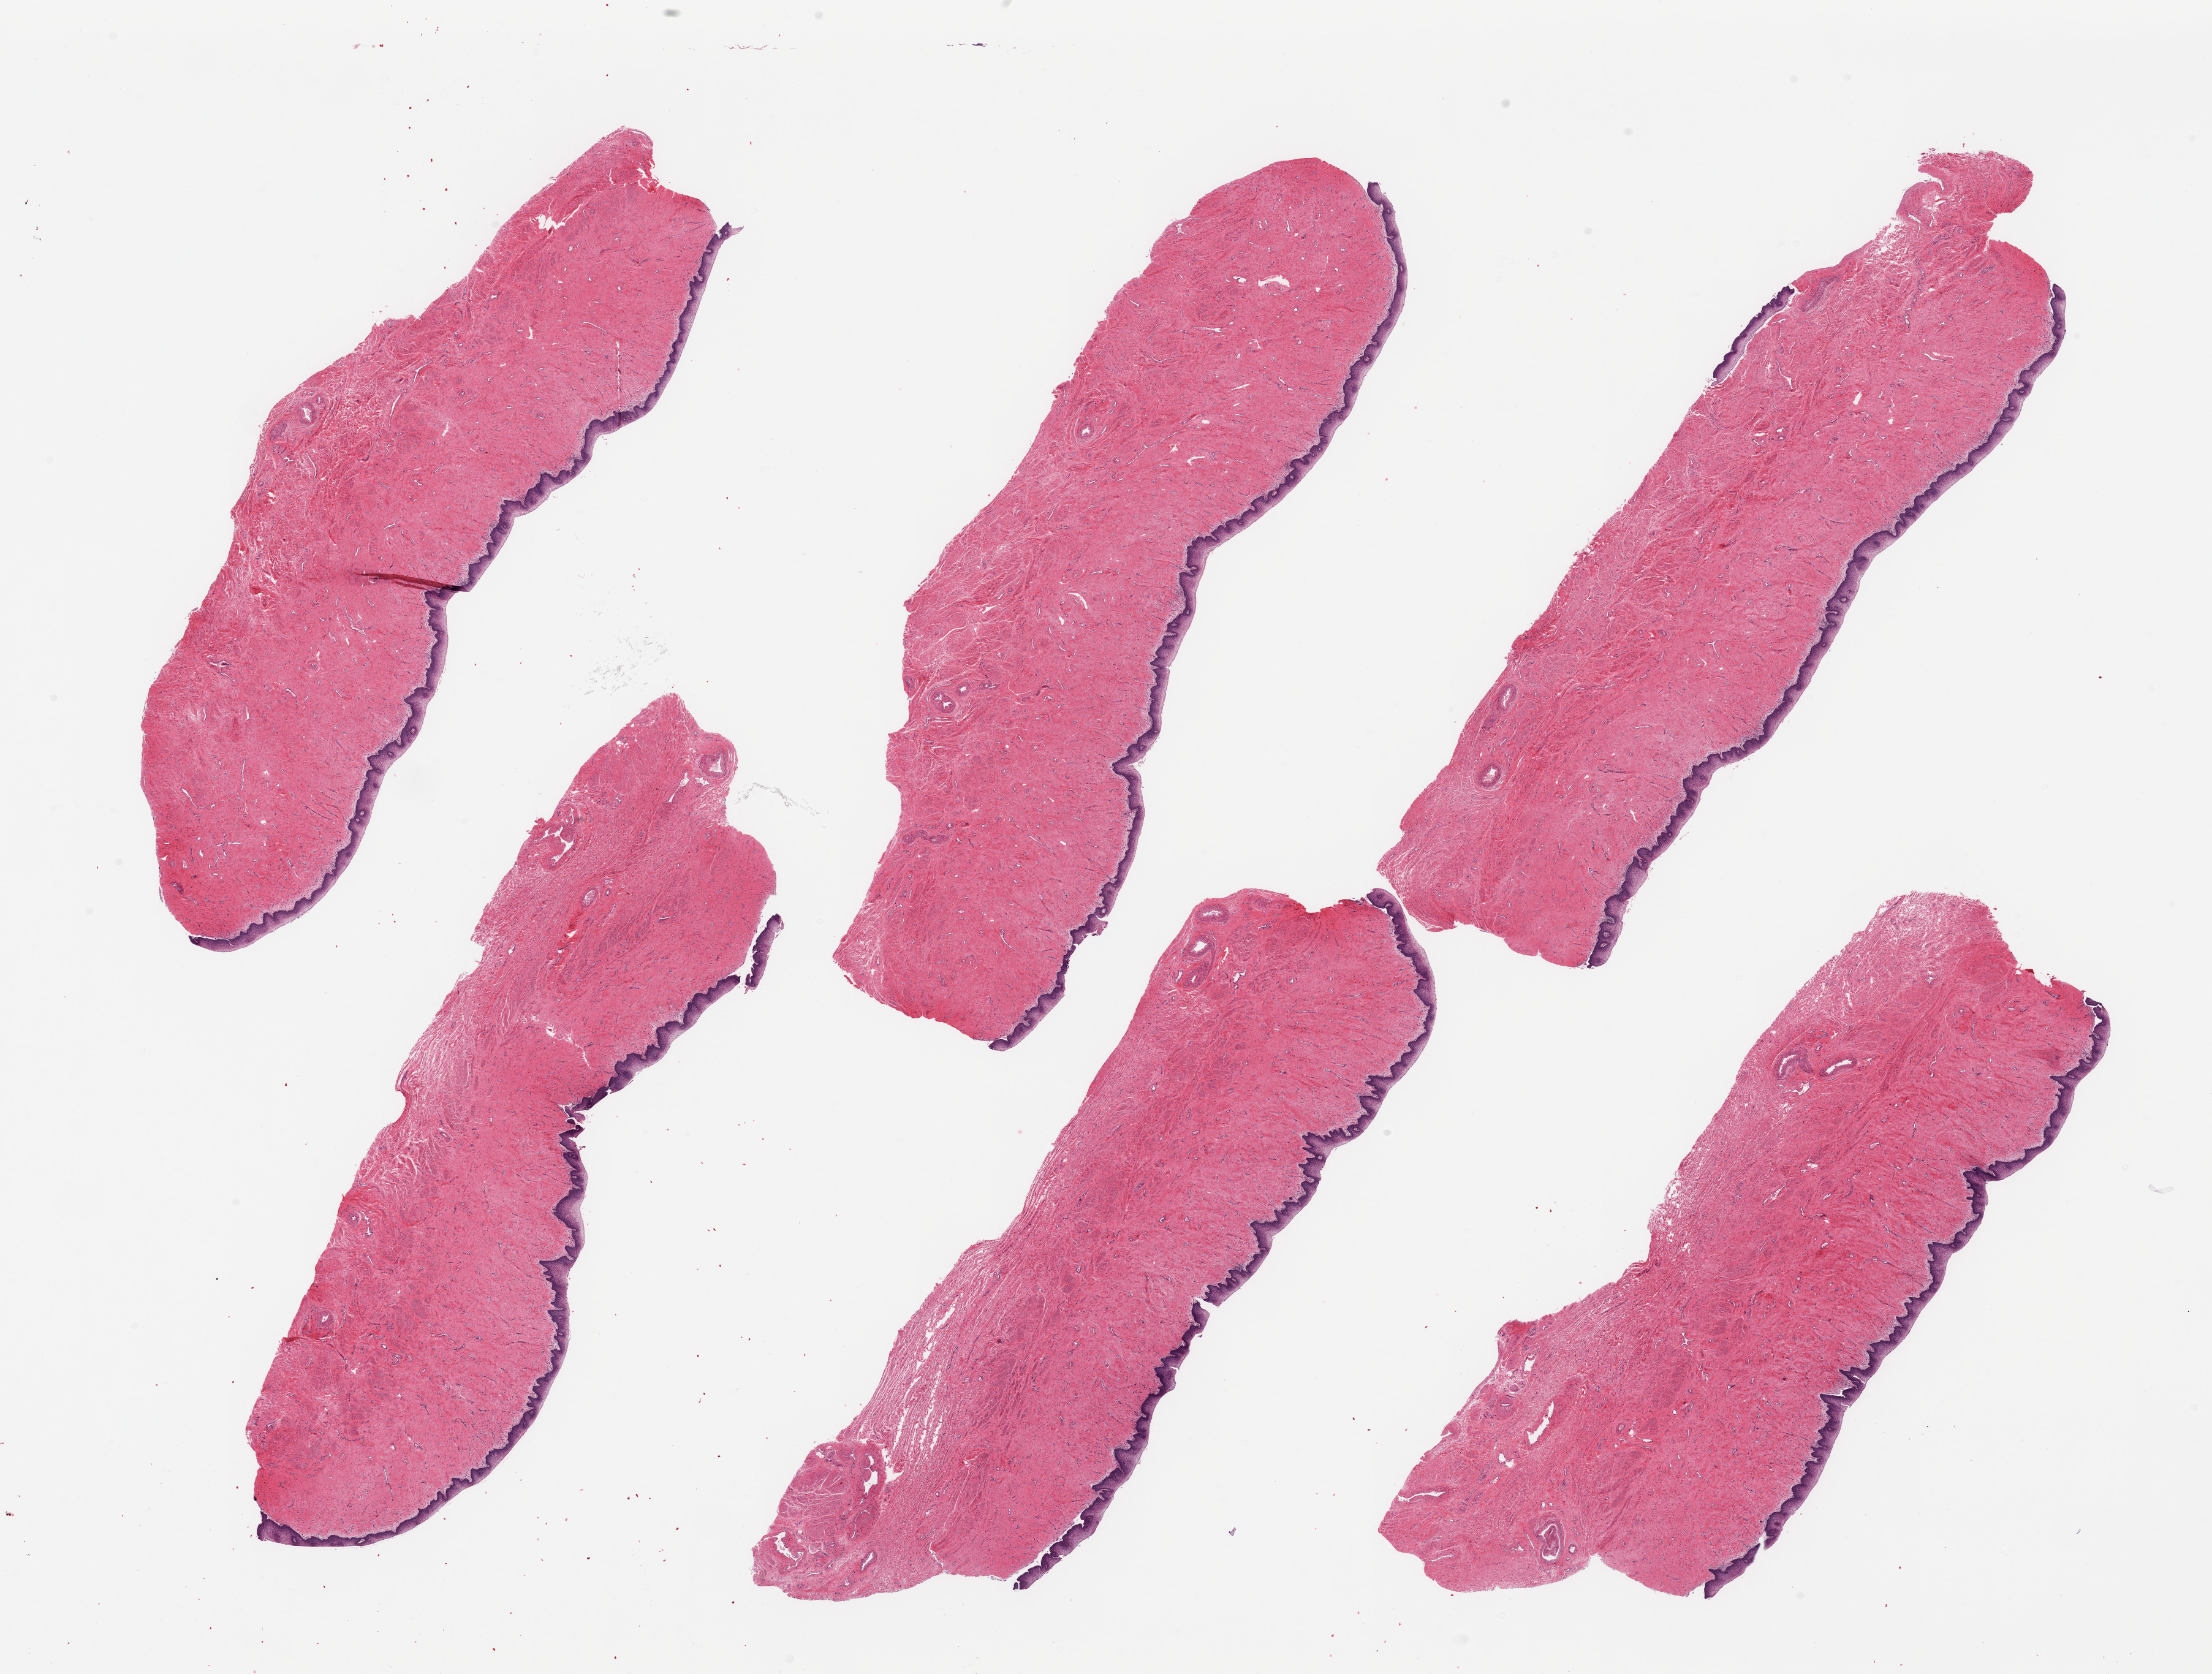
Digitized H&E-stained section — whole scanned area (about 28.5 x 21.6 mm) shown as a low-resolution overview; PAXgene-fixed paraffin-embedded (PFPE) section; target tissue: vagina; tissue donor sample. Female donor.
- review note (as recorded): 6 pieces, squamous epithelium is ~0.22mm, ~5-10% thickness